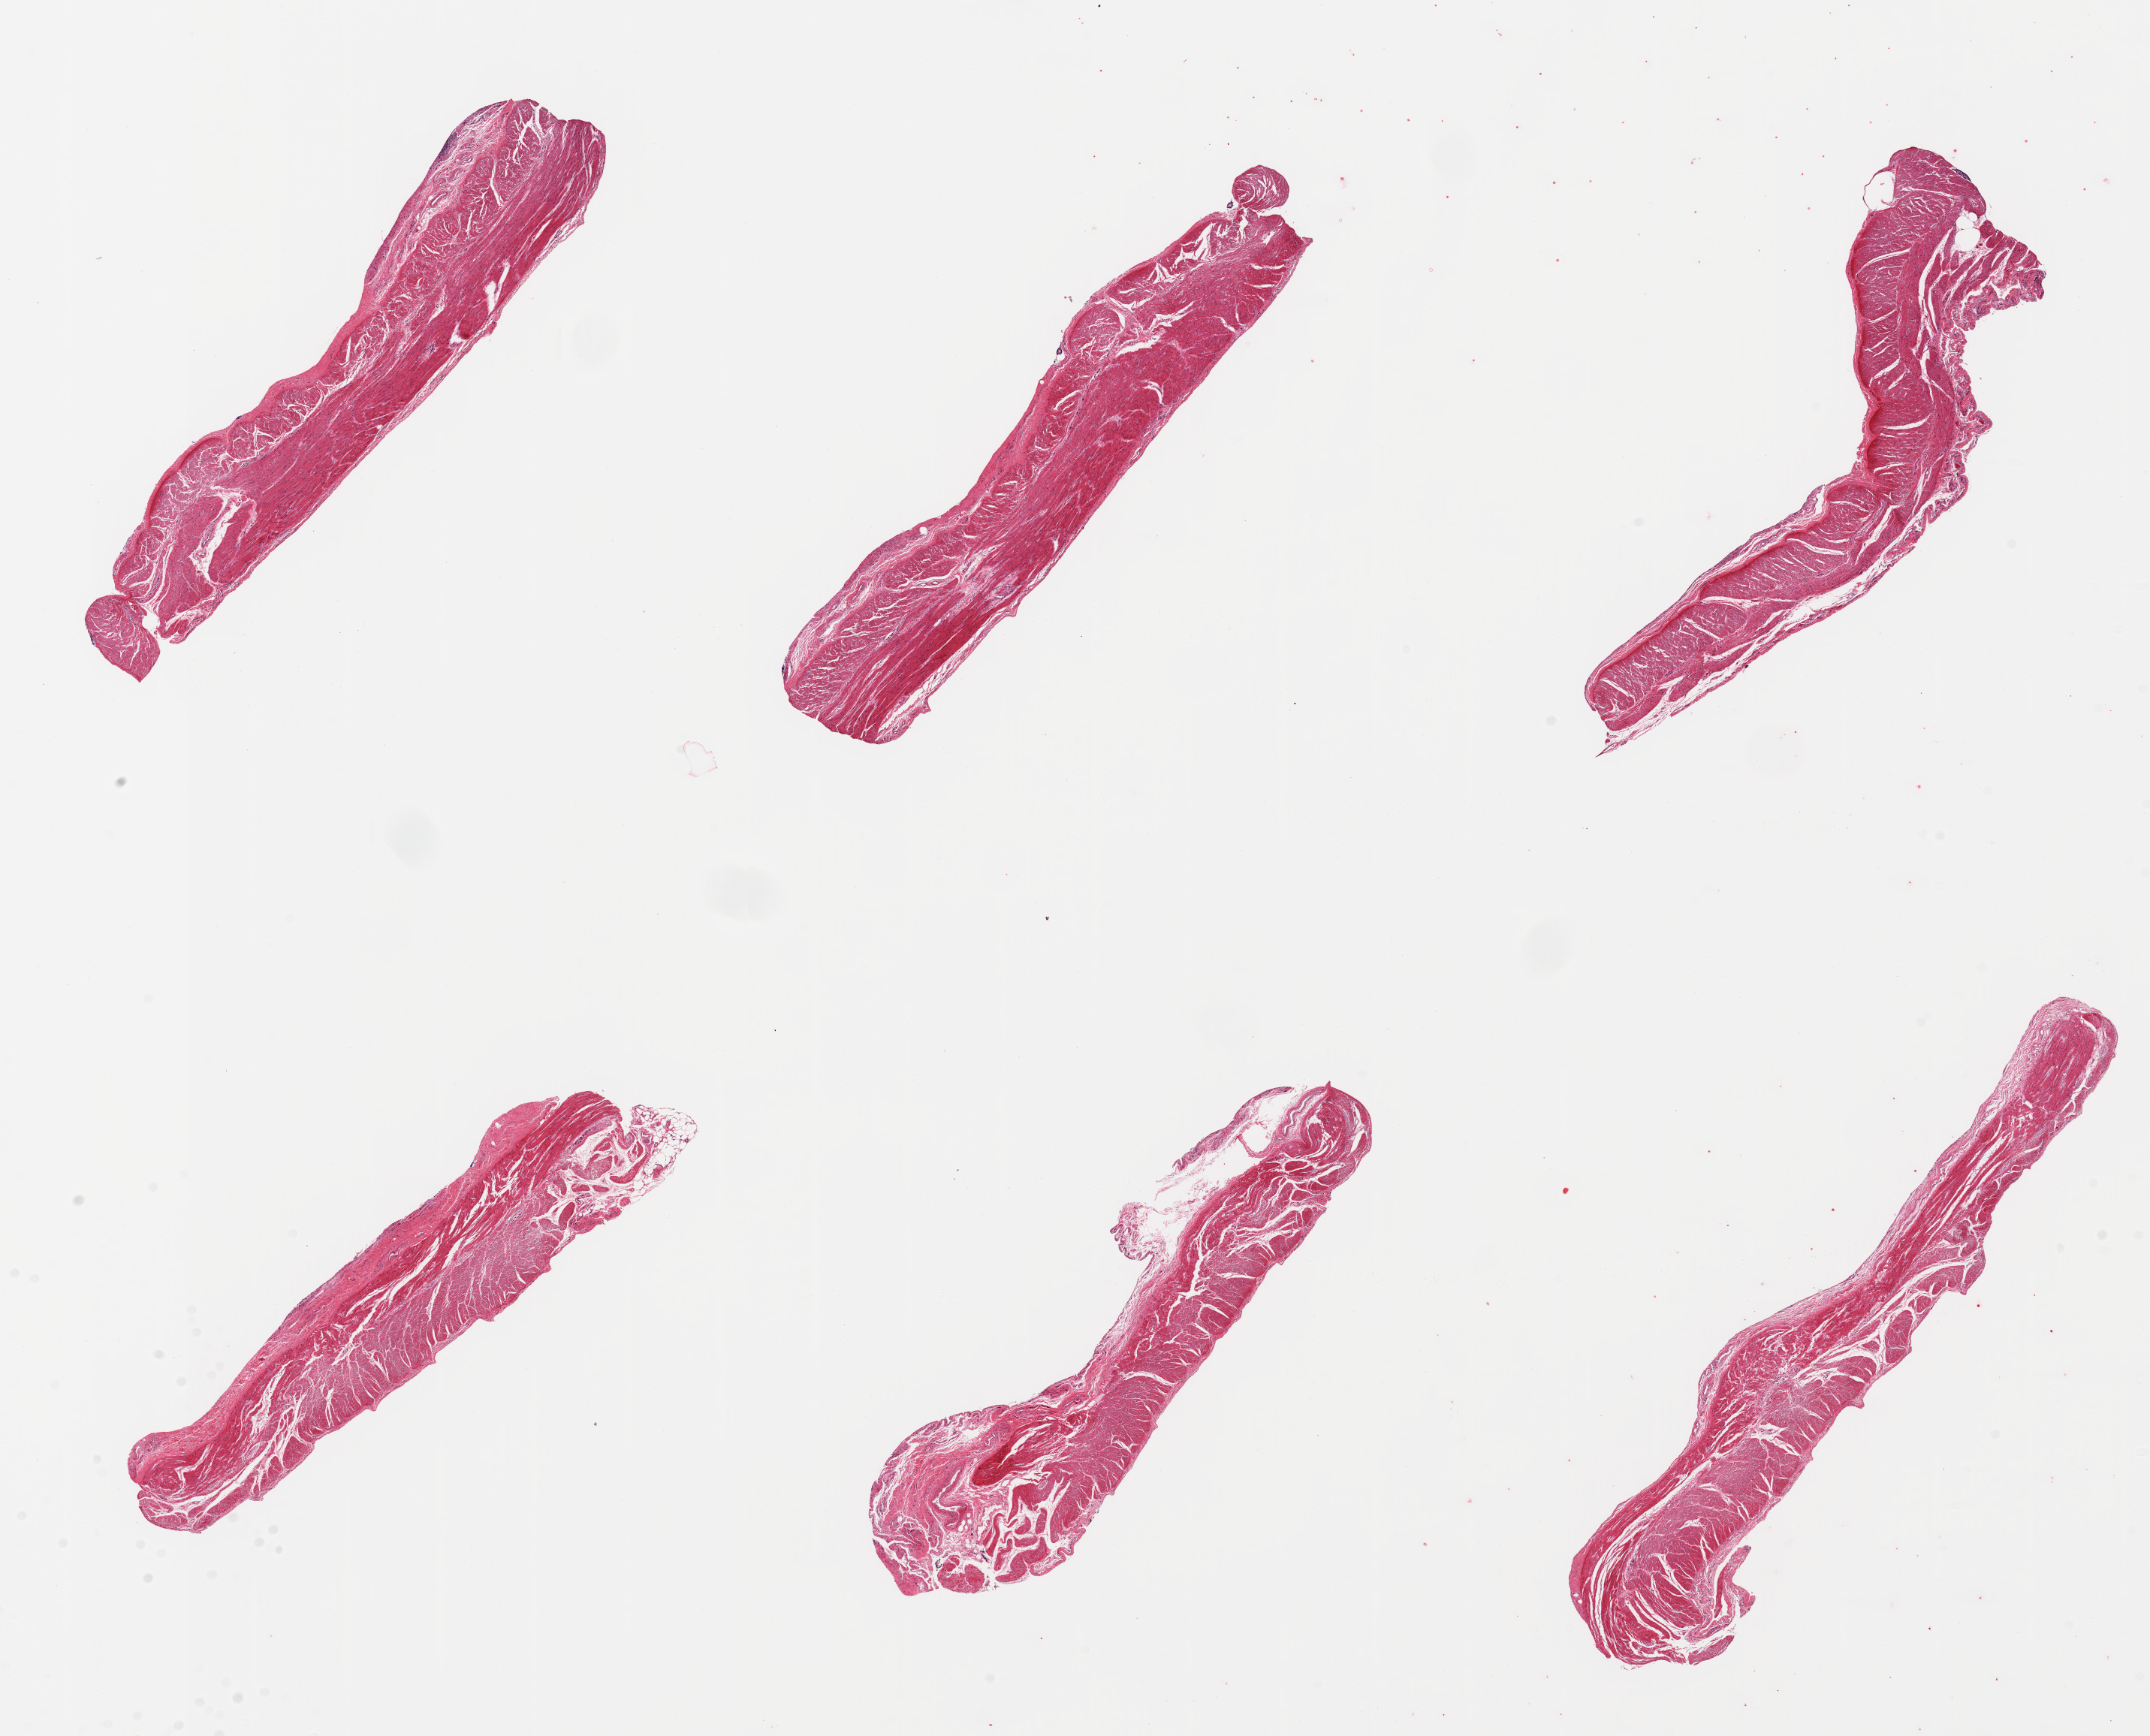
H&E whole-slide image, low-resolution overview of the scanned area, about 22.6 x 18.3 mm (slide scanned at 20x); PAXgene-fixed, paraffin-embedded tissue; target tissue: sigmoid colon; donor tissue sample. Donor: male.
• review note (as recorded): 6 pieces, confirmed target muscularis